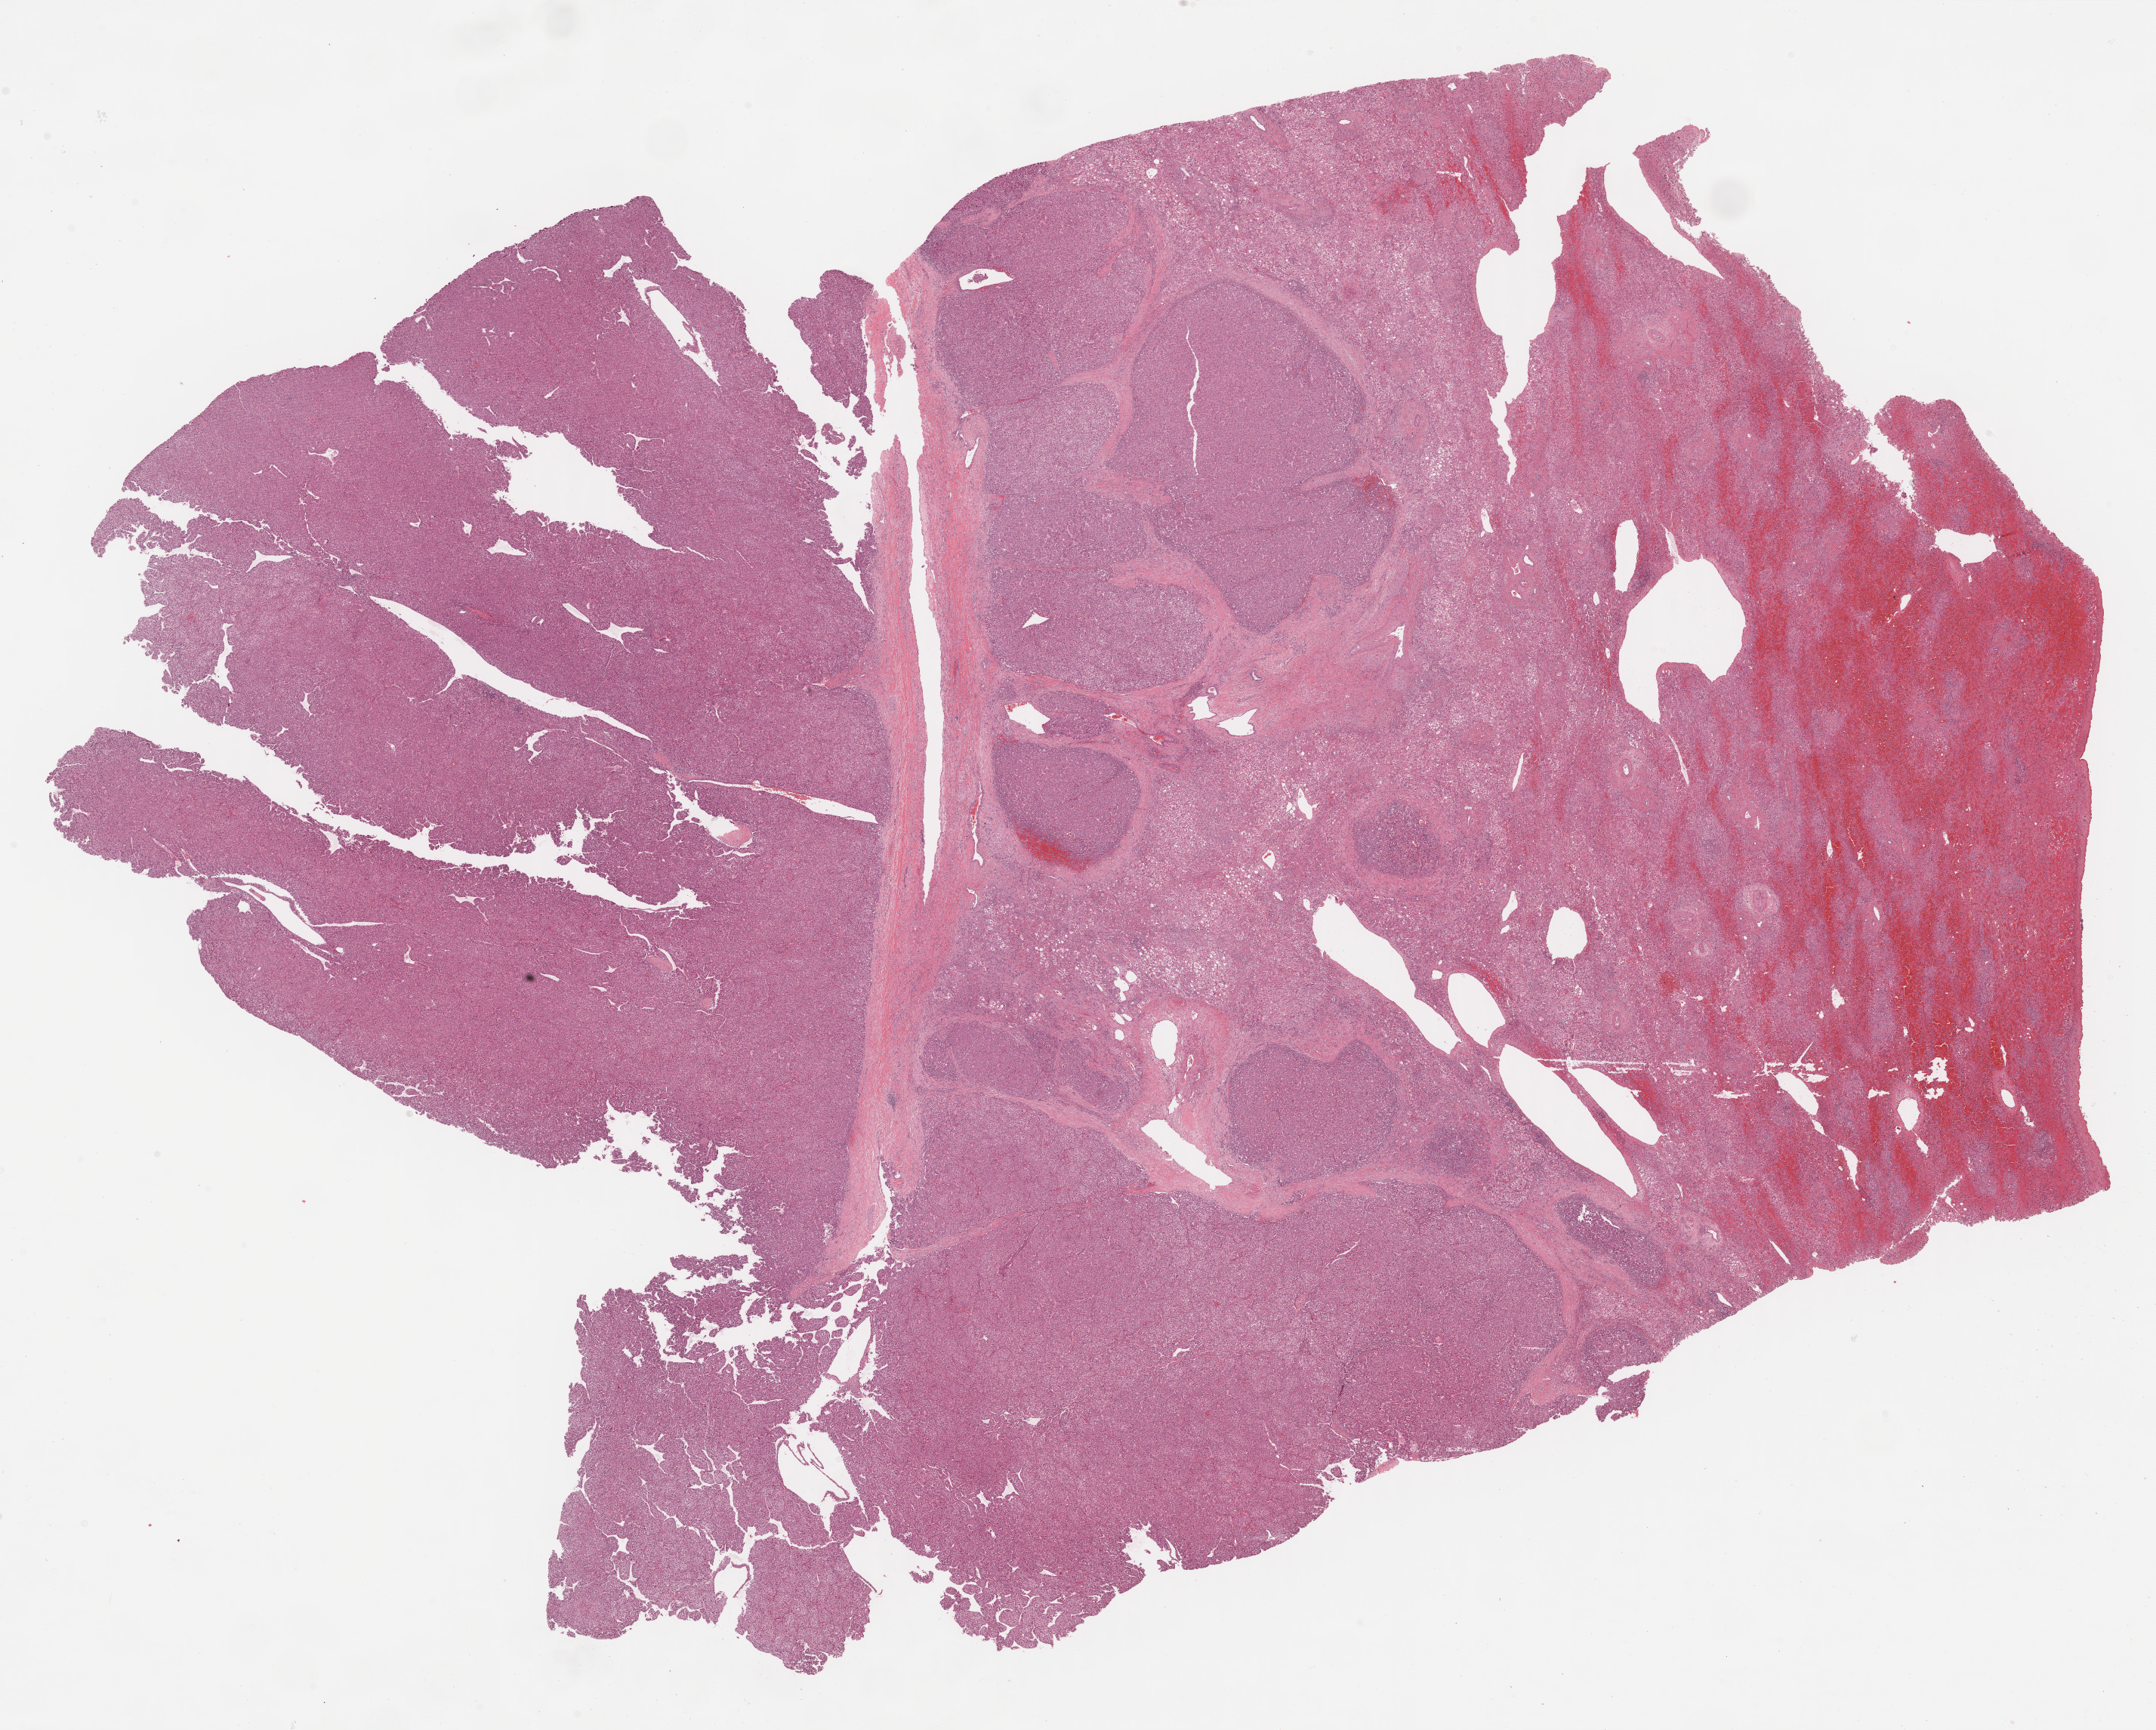
Whole-slide histology image, Hematoxylin and eosin (H&E) stained, a low-resolution overview of the entire scanned area, about 23.1 x 18.5 mm (from a 40x scan). Formalin-fixed paraffin-embedded (FFPE) diagnostic section. Sample: primary tumour, liver. Female, age 56 years at initial diagnosis. Histologic grade: G3 (poorly differentiated).
AJCC pathologic stage: I. TNM: T1 N0 M0. Diagnosis: Hepatocellular carcinoma, NOS.